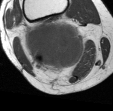
MRI of an extremity soft-tissue mass, one axial slice; position 32 of 45 along the scan axis; MR volume resampled by the dataset authors to the PET/CT grid (not the native acquisition matrix); 3.27 mm slice thickness; 113 × 111 image matrix. Female patient. From the clinical record (not read from this slice): histological type: liposarcoma; site of the primary tumour: right thigh.
Outlined on this slice (expert contour drawn on MRI and transferred to this co-registered scan by the dataset authors):
- gross tumour volume (mass): box from (x=21, y=17) to (x=86, y=73) px